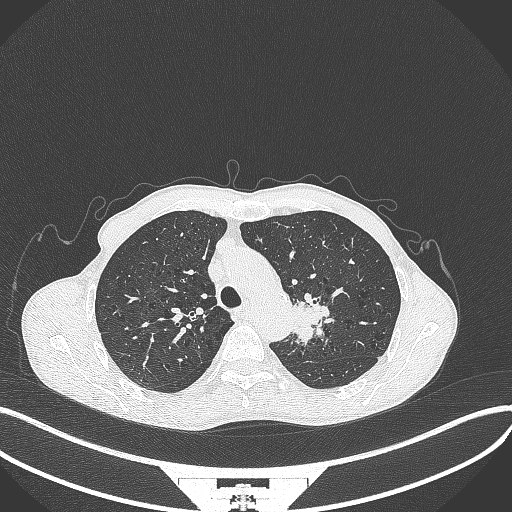
Chest CT, one axial slice. Position 310 of 386 along the scan axis. Reconstruction kernel B70f. Lung window (W 1500 / L -600 HU). 1 mm slice thickness. 512 × 512 image matrix. Male patient, age 65 years. Case-level facts recorded for this patient, not image findings: clinical TNM (as recorded): T2b N0 M0; histopathological grade: G2.
Structures marked on this image (rectangle marked by the reading radiologist):
- lung tumour (recorded histology: adenocarcinoma): bounding box [x1, y1, x2, y2] px = [284, 289, 330, 348]